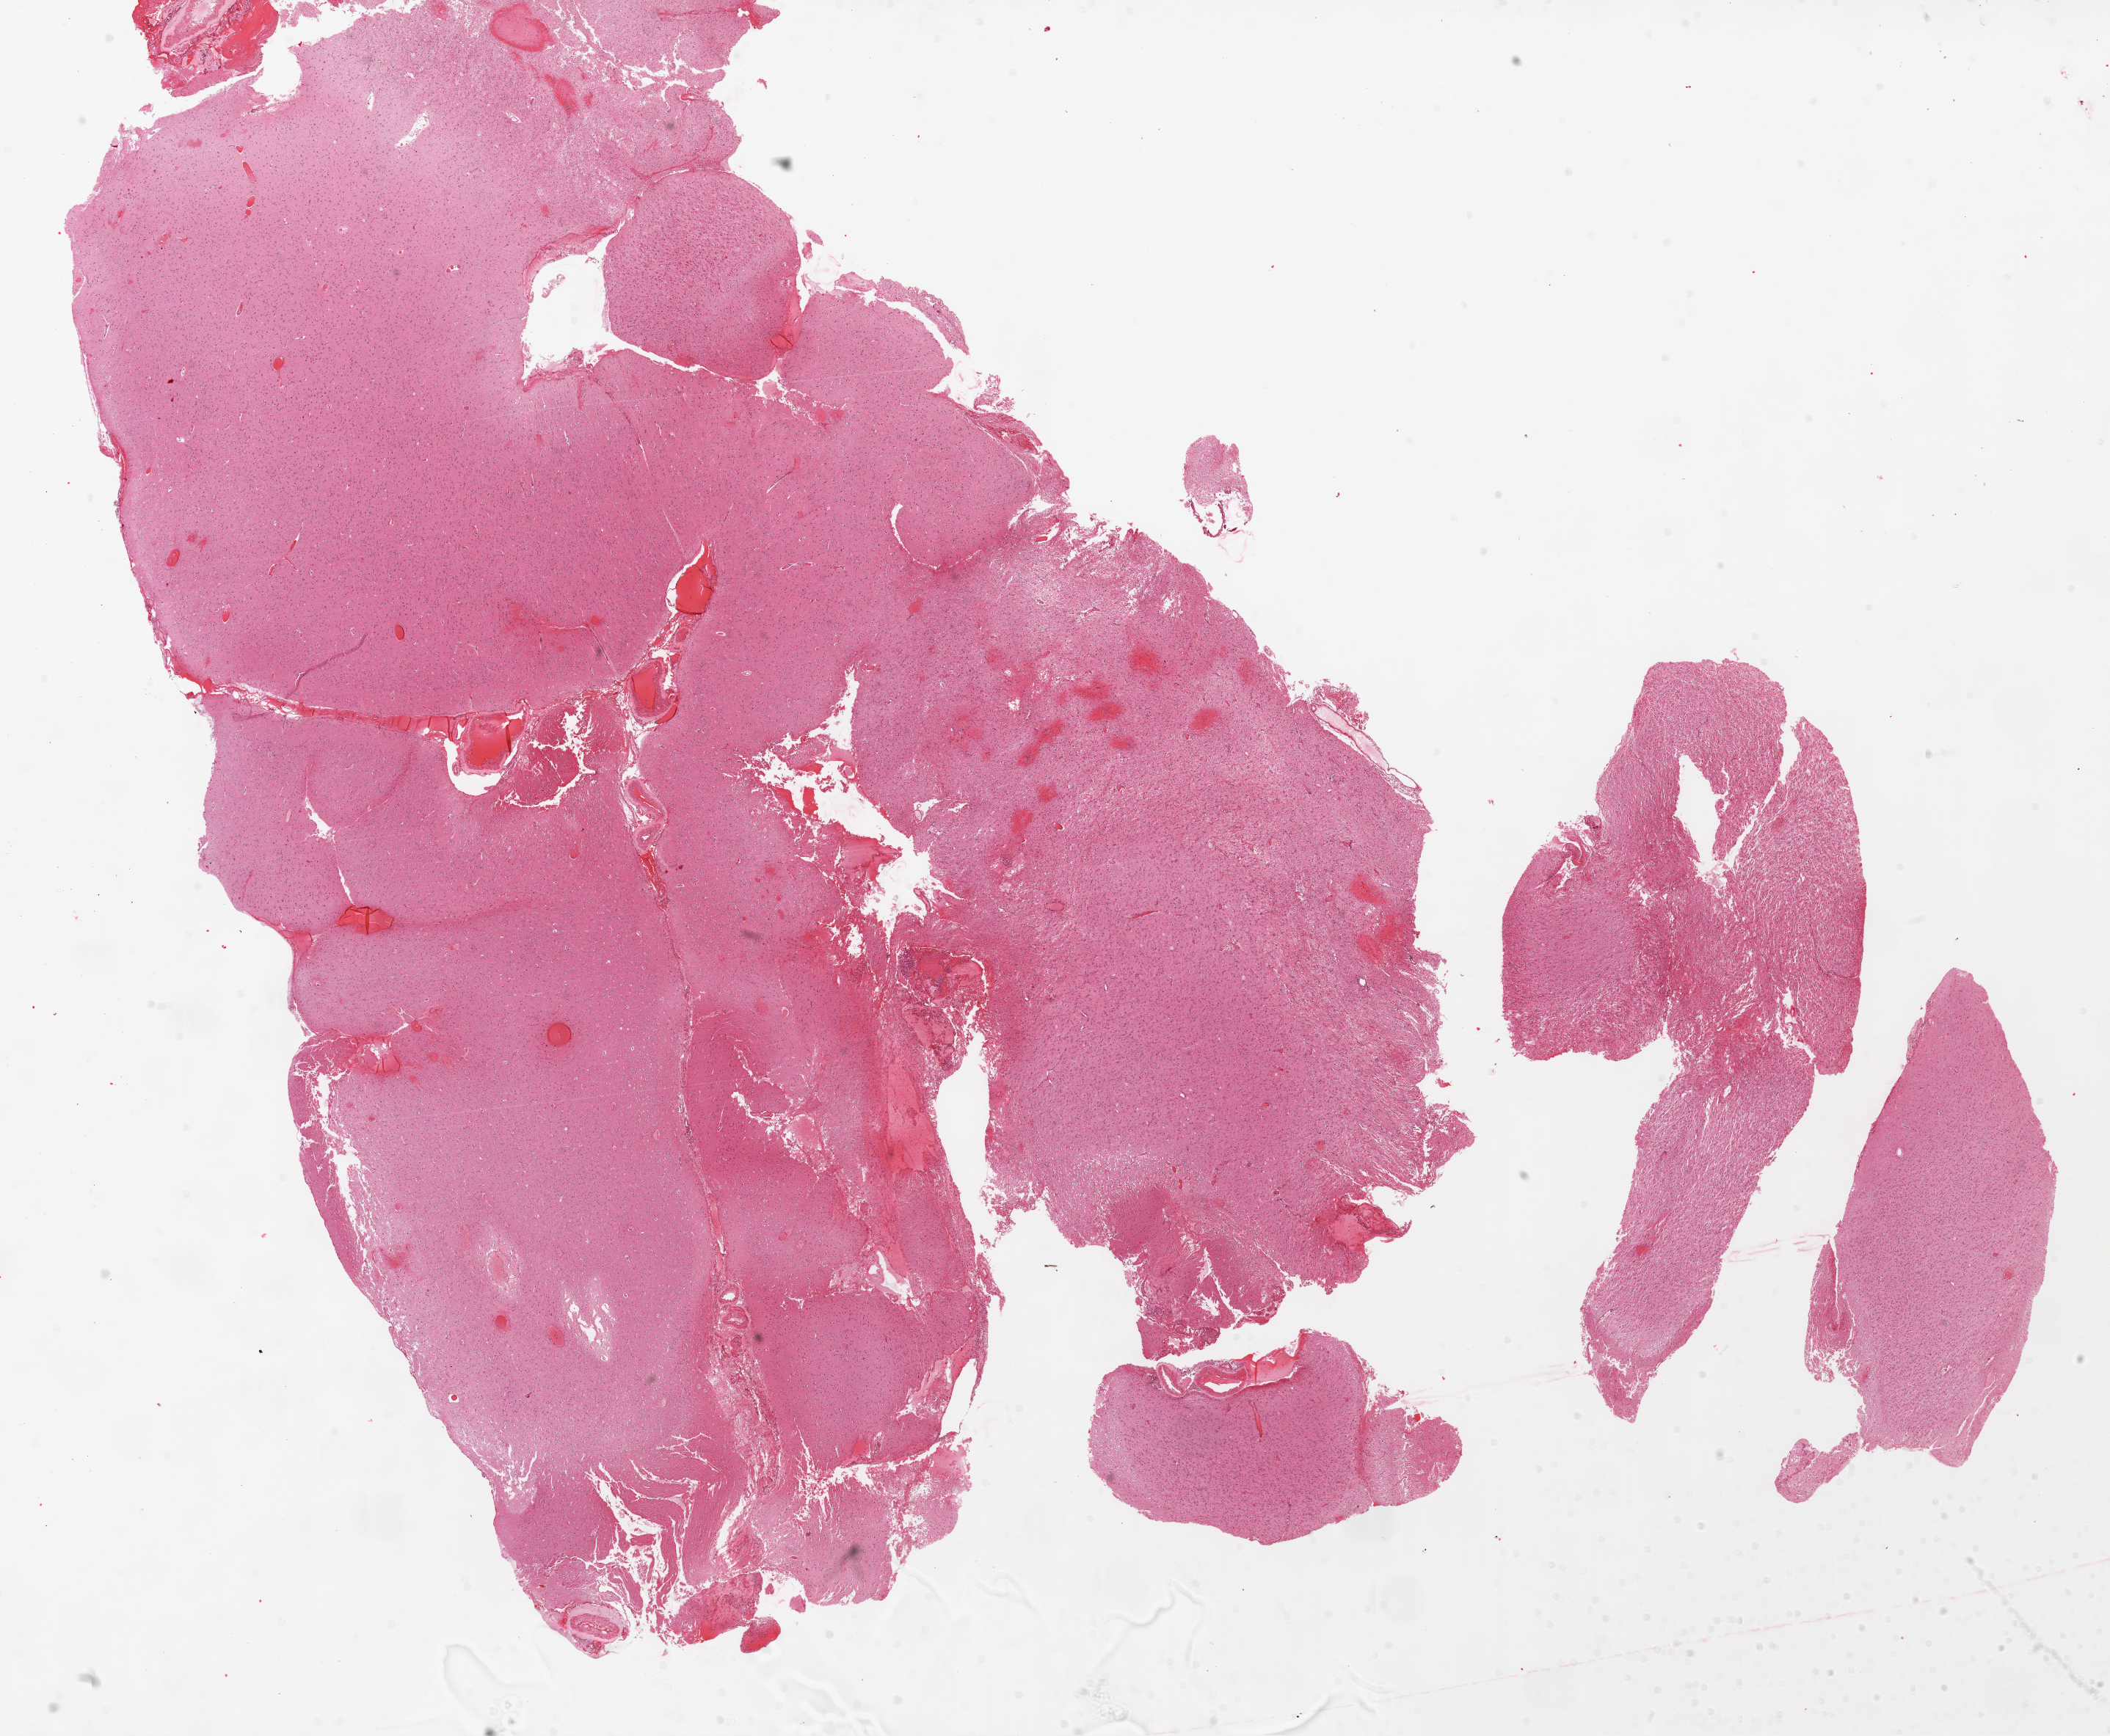
Whole-slide histology image, H&E-stained — low-resolution overview of the scanned area, about 23.1 x 19.0 mm (acquisition: 20x scan). Formalin-fixed paraffin-embedded (FFPE) diagnostic section. Brain, primary tumour sample. Female patient; age at initial diagnosis 59 years.
- histologic diagnosis: Glioblastoma